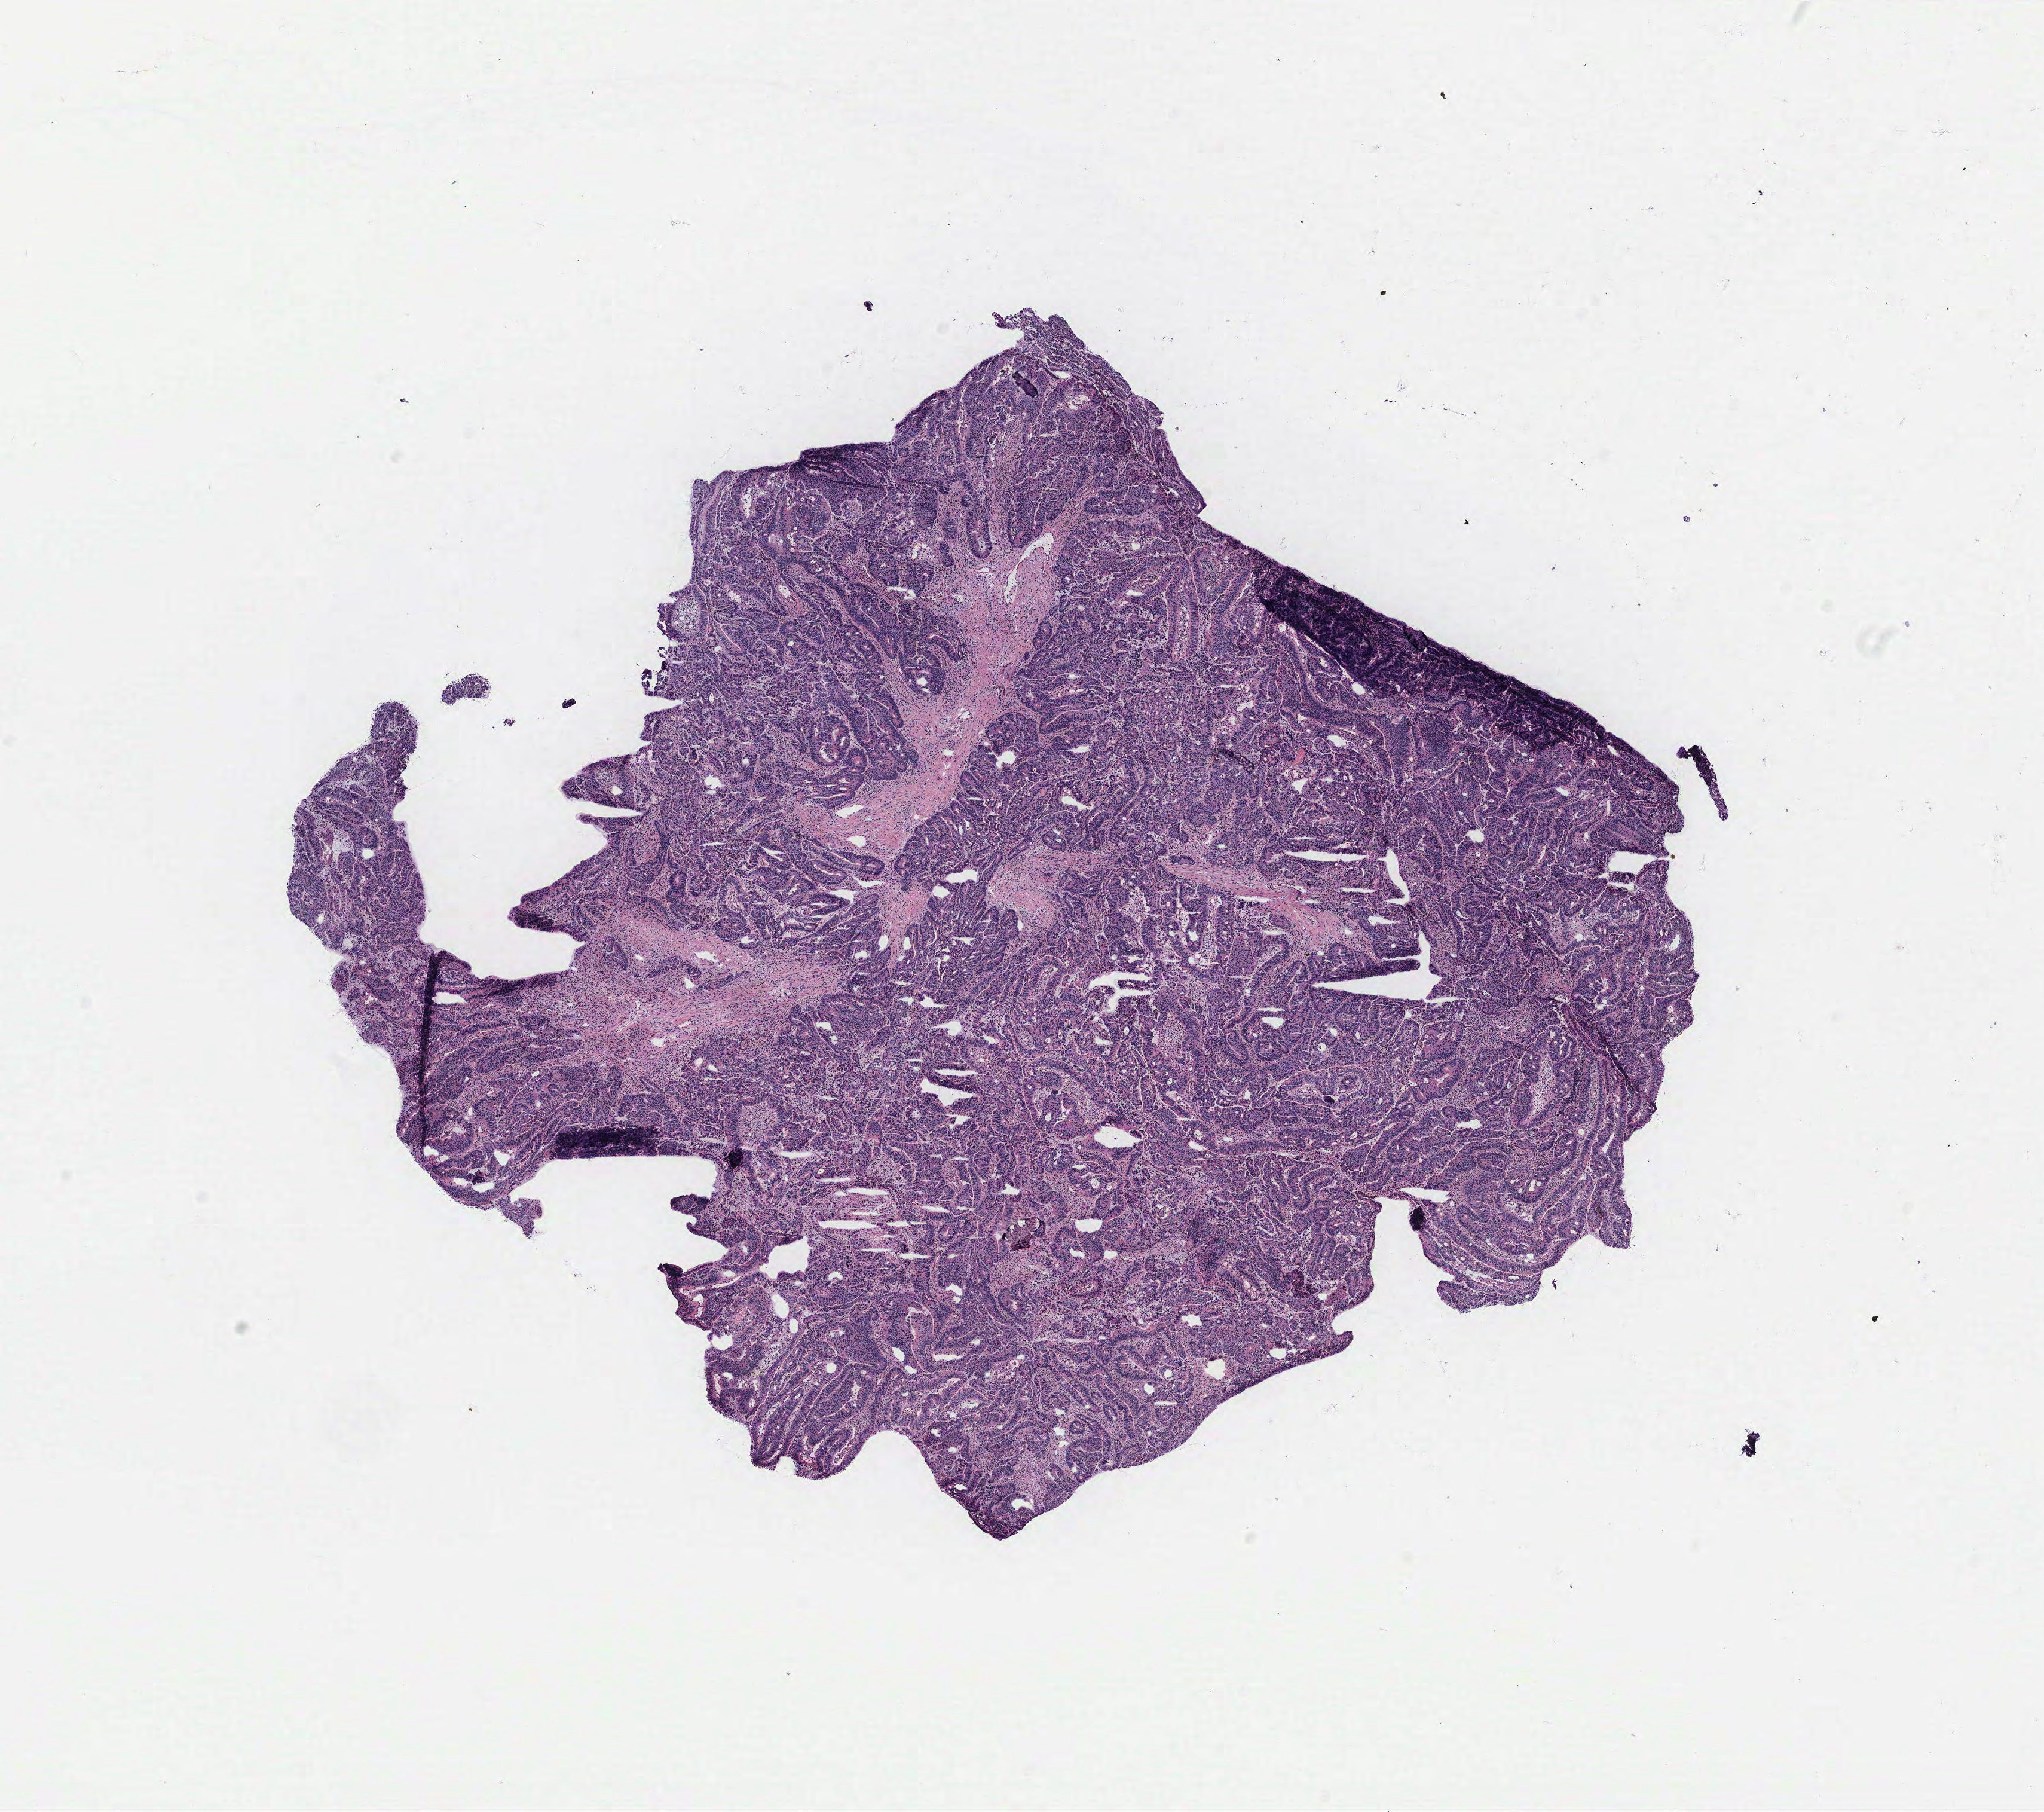
Digitized H&E tissue section (whole slide), a low-resolution overview of the entire scanned area, about 13.7 x 12.1 mm; normal (non-tumour) tissue sample, colon. 62-year-old male patient.
This section: normal (non-tumour) tissue from the same patient. Patient diagnosis: Adenocarcinoma, NOS.